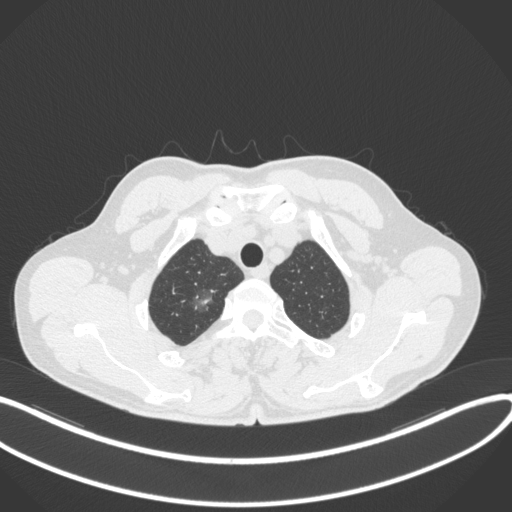
Chest CT, one axial slice. Slice 336 of 407 in the series (ordered by position). 120 kVp. Lung window (W 1500 / L -600 HU). 512 × 512 image matrix, field of view 400 × 400 mm. Patient: male, 58 years. From the clinical record (not read from this slice): clinical TNM (as recorded): T1c N0 M0.
Annotated regions visible in this slice (rectangle marked by the reading radiologist):
- lung tumour (recorded histology: adenocarcinoma): box from (x=190, y=283) to (x=216, y=316) px